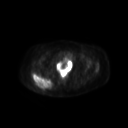
FDG PET of an extremity soft-tissue mass (from a PET/CT study), one axial slice; position 50 of 267 along the scan axis; 3.27 mm slice thickness; 128 × 128 image matrix, field of view 600 × 600 mm. Patient: female, 60 years. From the clinical record (not read from this slice): histological type: spindle cell suggestive of myxofibrosarcoma; grade: intermediate; site of the primary tumour: right buttock.
Outlined on this slice (expert contour drawn on MRI and transferred to this co-registered scan by the dataset authors):
- gross tumour volume (mass): bounding box (x1, y1, x2, y2) in pixels: (32, 72, 53, 88)